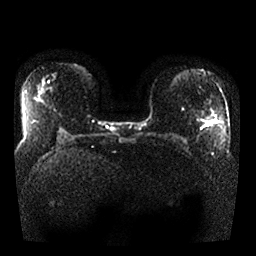
Breast MRI, one axial slice; position 16 of 25 along the scan axis; diffusion-weighted series; image 2 of 4 stored at this slice position (different b-values; order by instance number); 1.5 T; 4 mm slice thickness; 256 × 256 image matrix. Female patient.
Outlined on this slice (outlined manually by an expert reader):
- tumour on diffusion-weighted imaging: bounding box <207,122,209,126> (left, top, right, bottom; pixels)